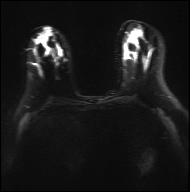
Breast MRI, one axial slice. Slice 17 of 36 in the series (ordered by position). Diffusion-weighted series; image 2 of 4 stored at this slice position (different b-values; order by instance number). 3 T. 4 mm slice thickness. 190 × 192 image matrix, field of view 317 × 320 mm. Female patient.
Annotated regions visible in this slice (outlined manually by an expert reader):
- tumour on diffusion-weighted imaging: bounding box (x1, y1, x2, y2) in pixels: (64, 30, 82, 36)